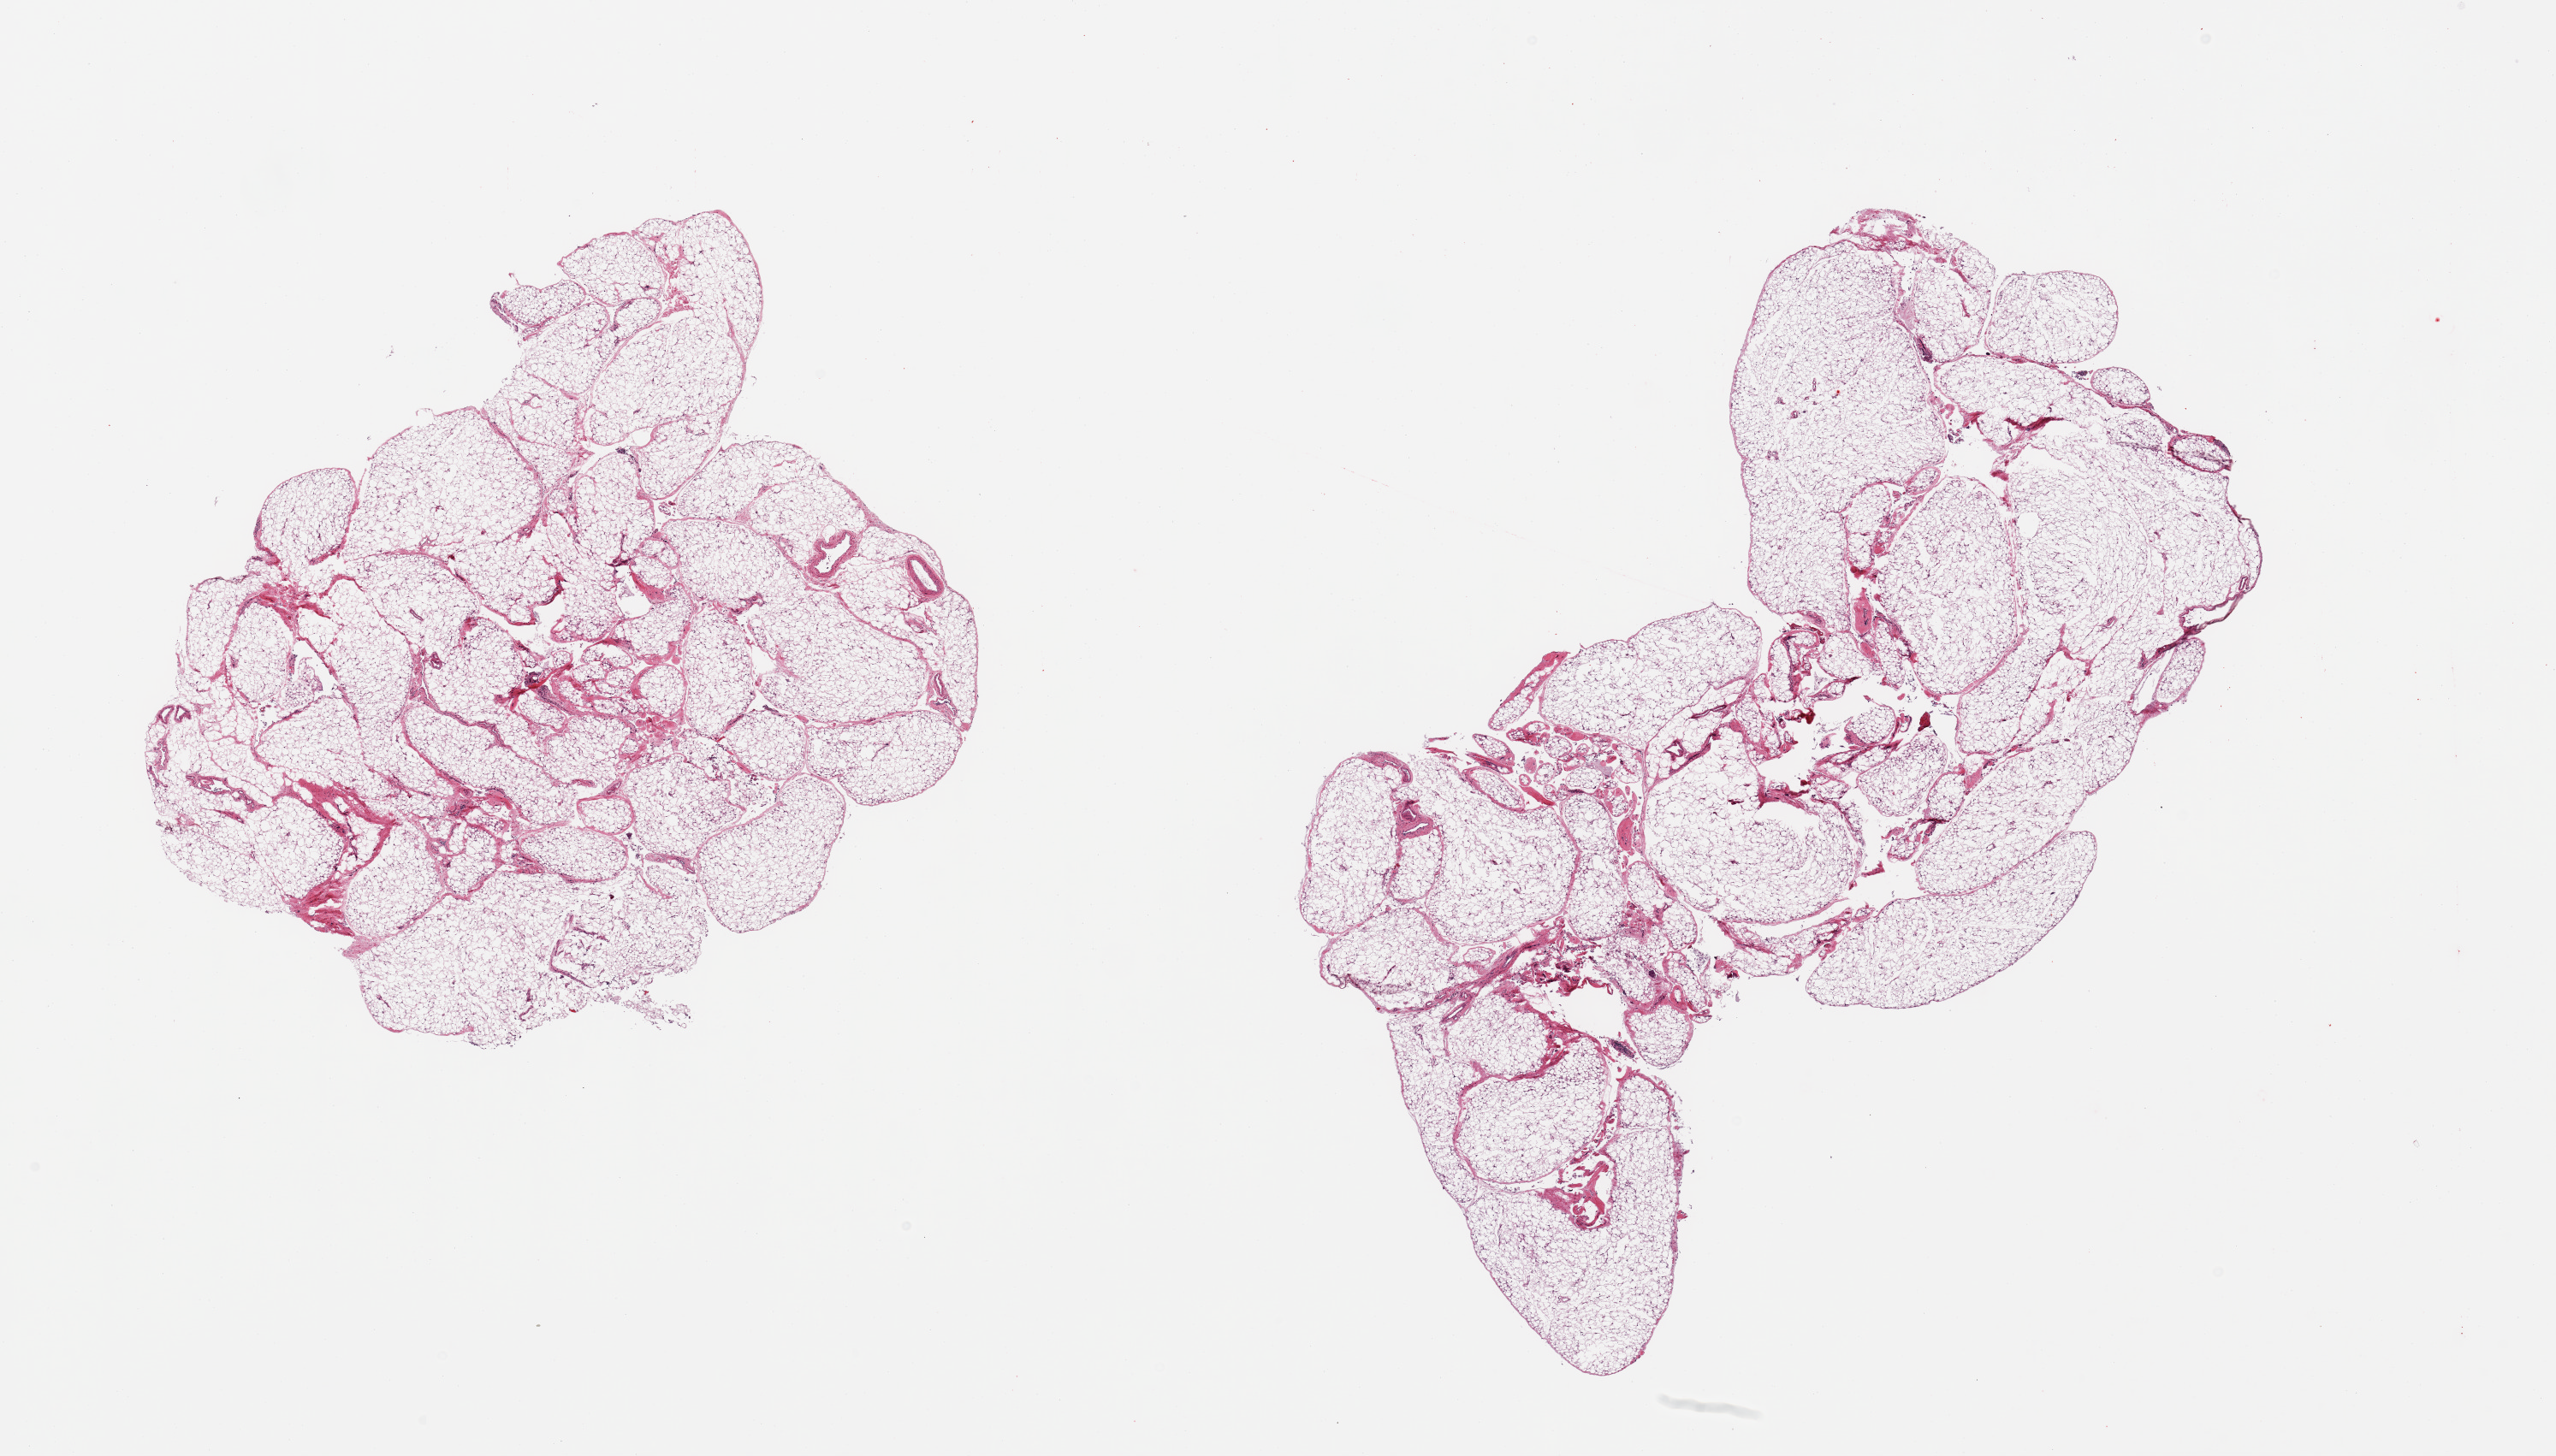
H&E whole-slide image — whole scanned area (about 23.6 x 13.5 mm, acquisition: 20x scan) shown as a low-resolution overview. PAXgene-fixed, paraffin-embedded tissue. Sampled site (target tissue): omentum. Tissue donor sample.
Reviewer comment on this tissue sample: 2 pieces; mature adipose tissue with fibrovascular septa.